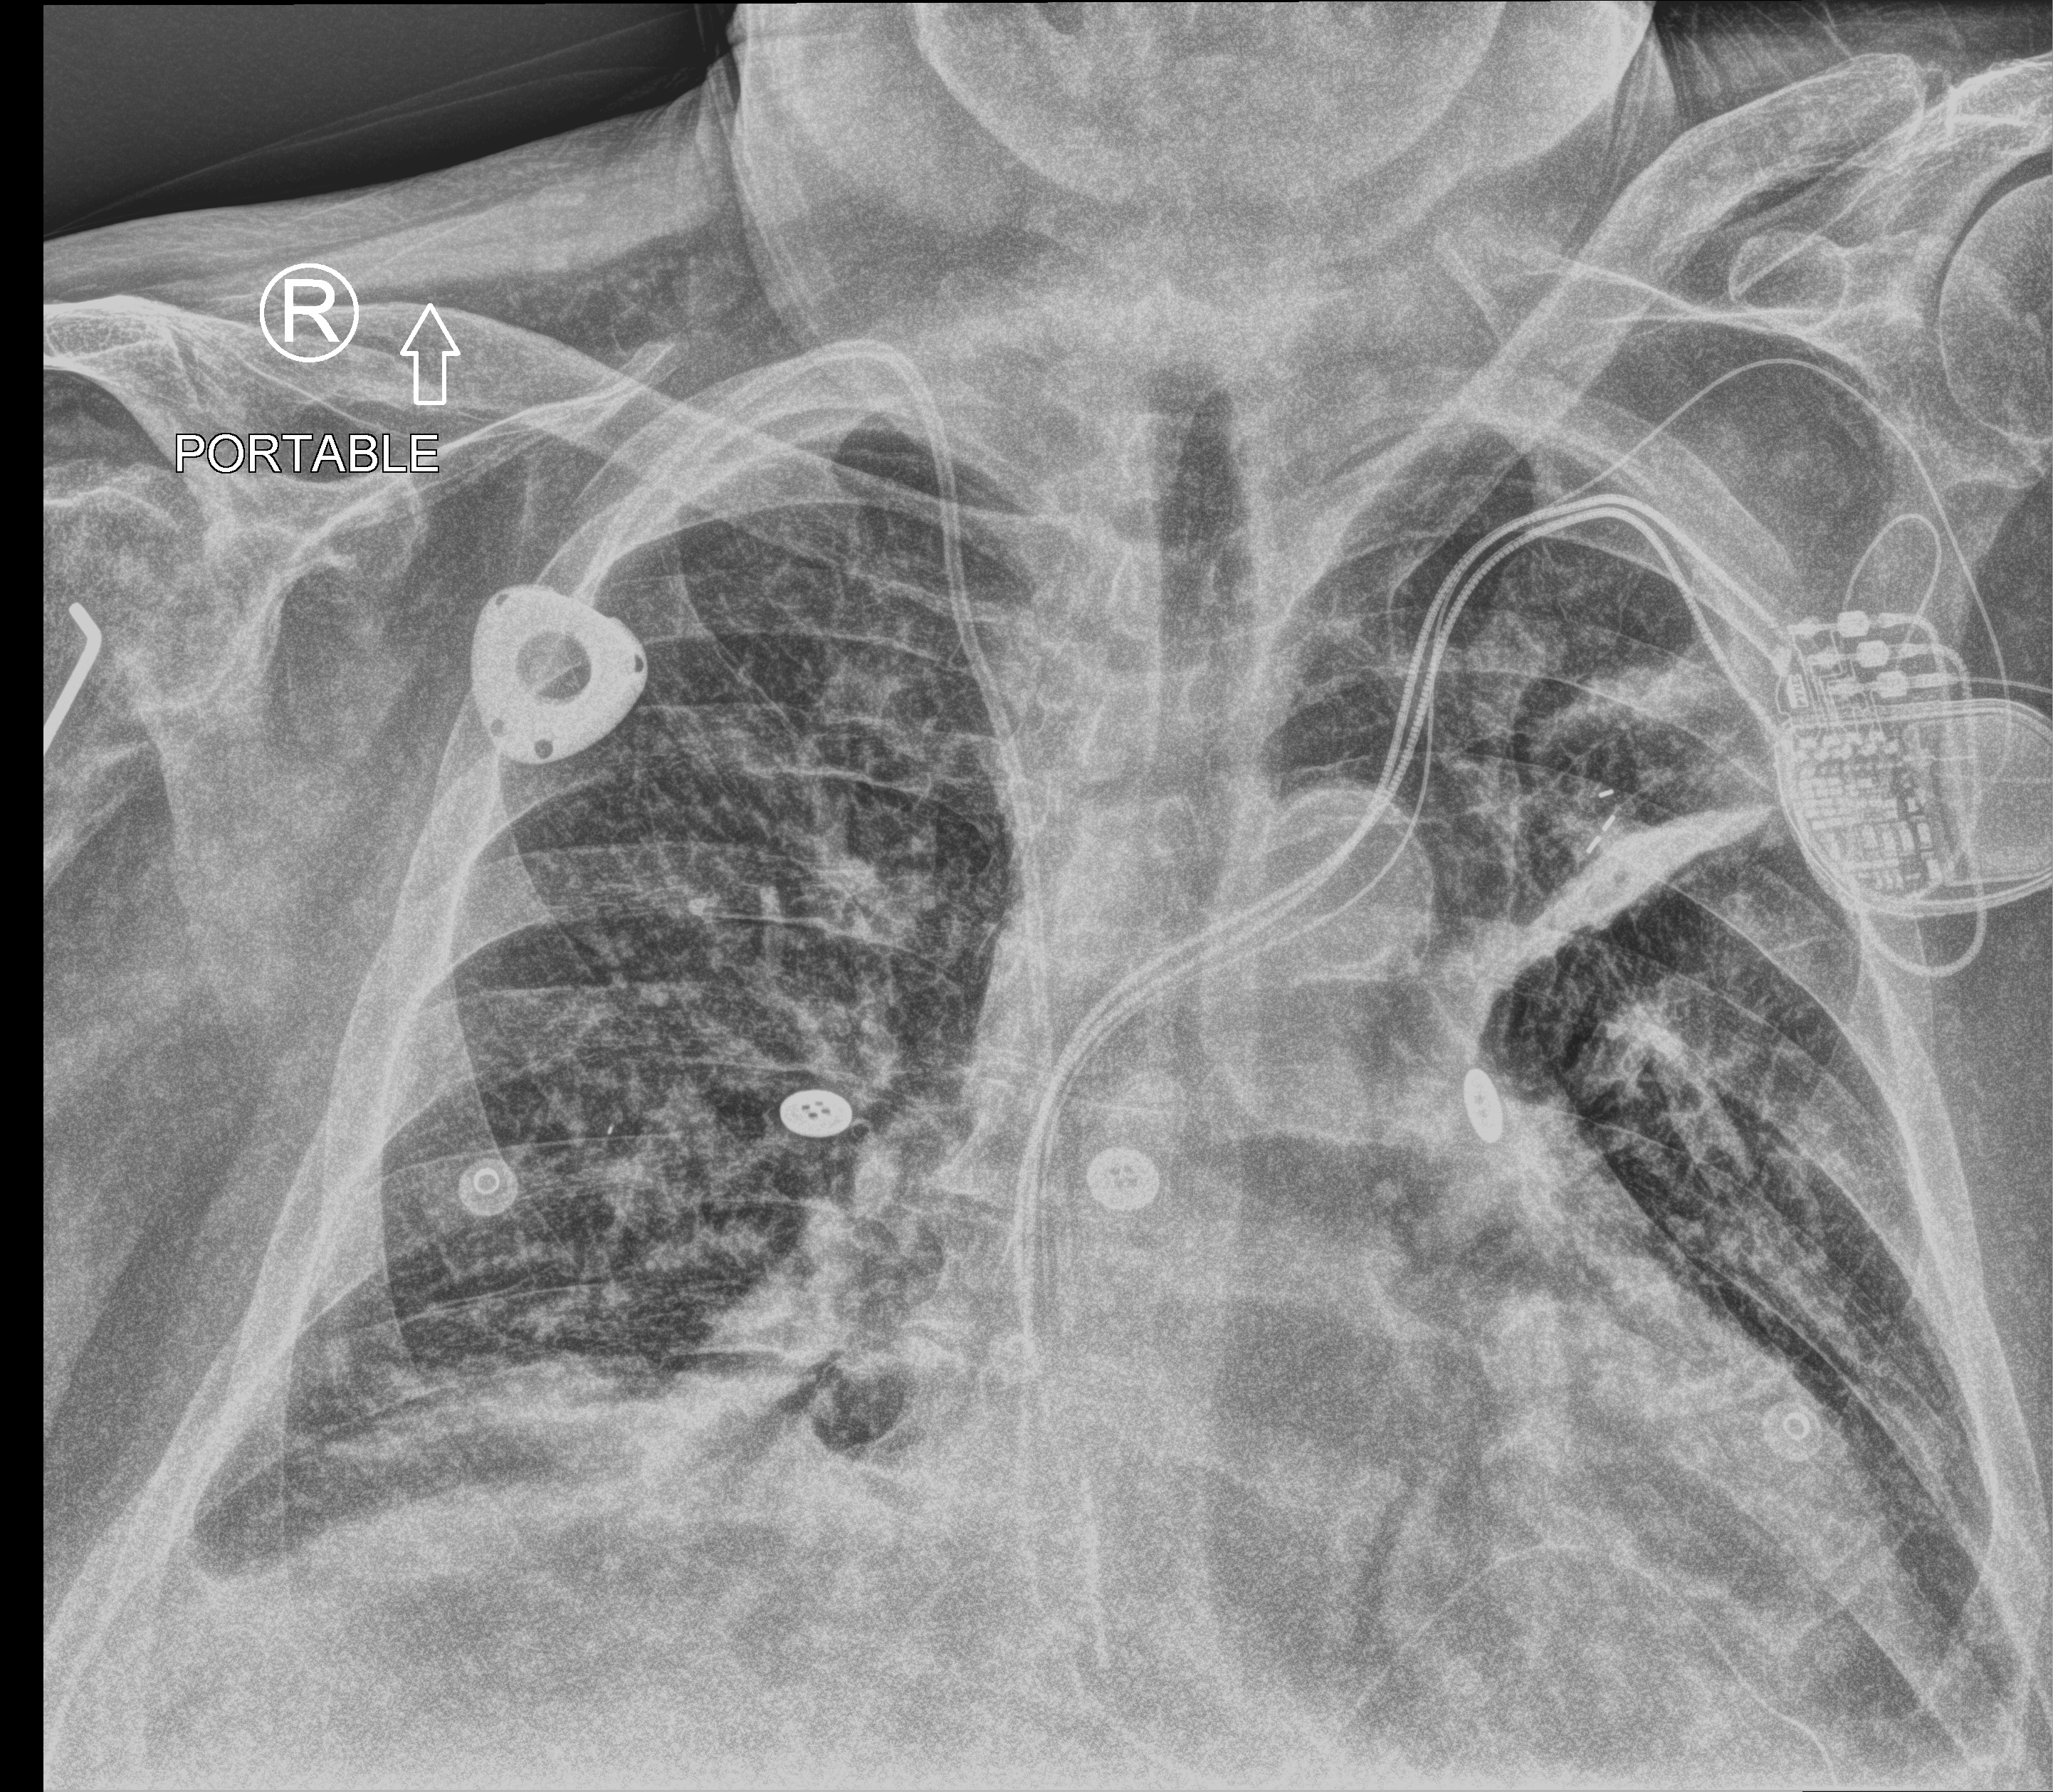
Bedside chest radiograph (computed radiography); anteroposterior (AP) projection. Male patient hospitalised with COVID-19, age 60–74 years.
Hospital-stay facts (about this admission, not read from this image; timing relative to this image not recorded): admitted to intensive care during this hospital stay: yes; mechanically ventilated during this hospital stay: no; length of hospital stay: 20 days.